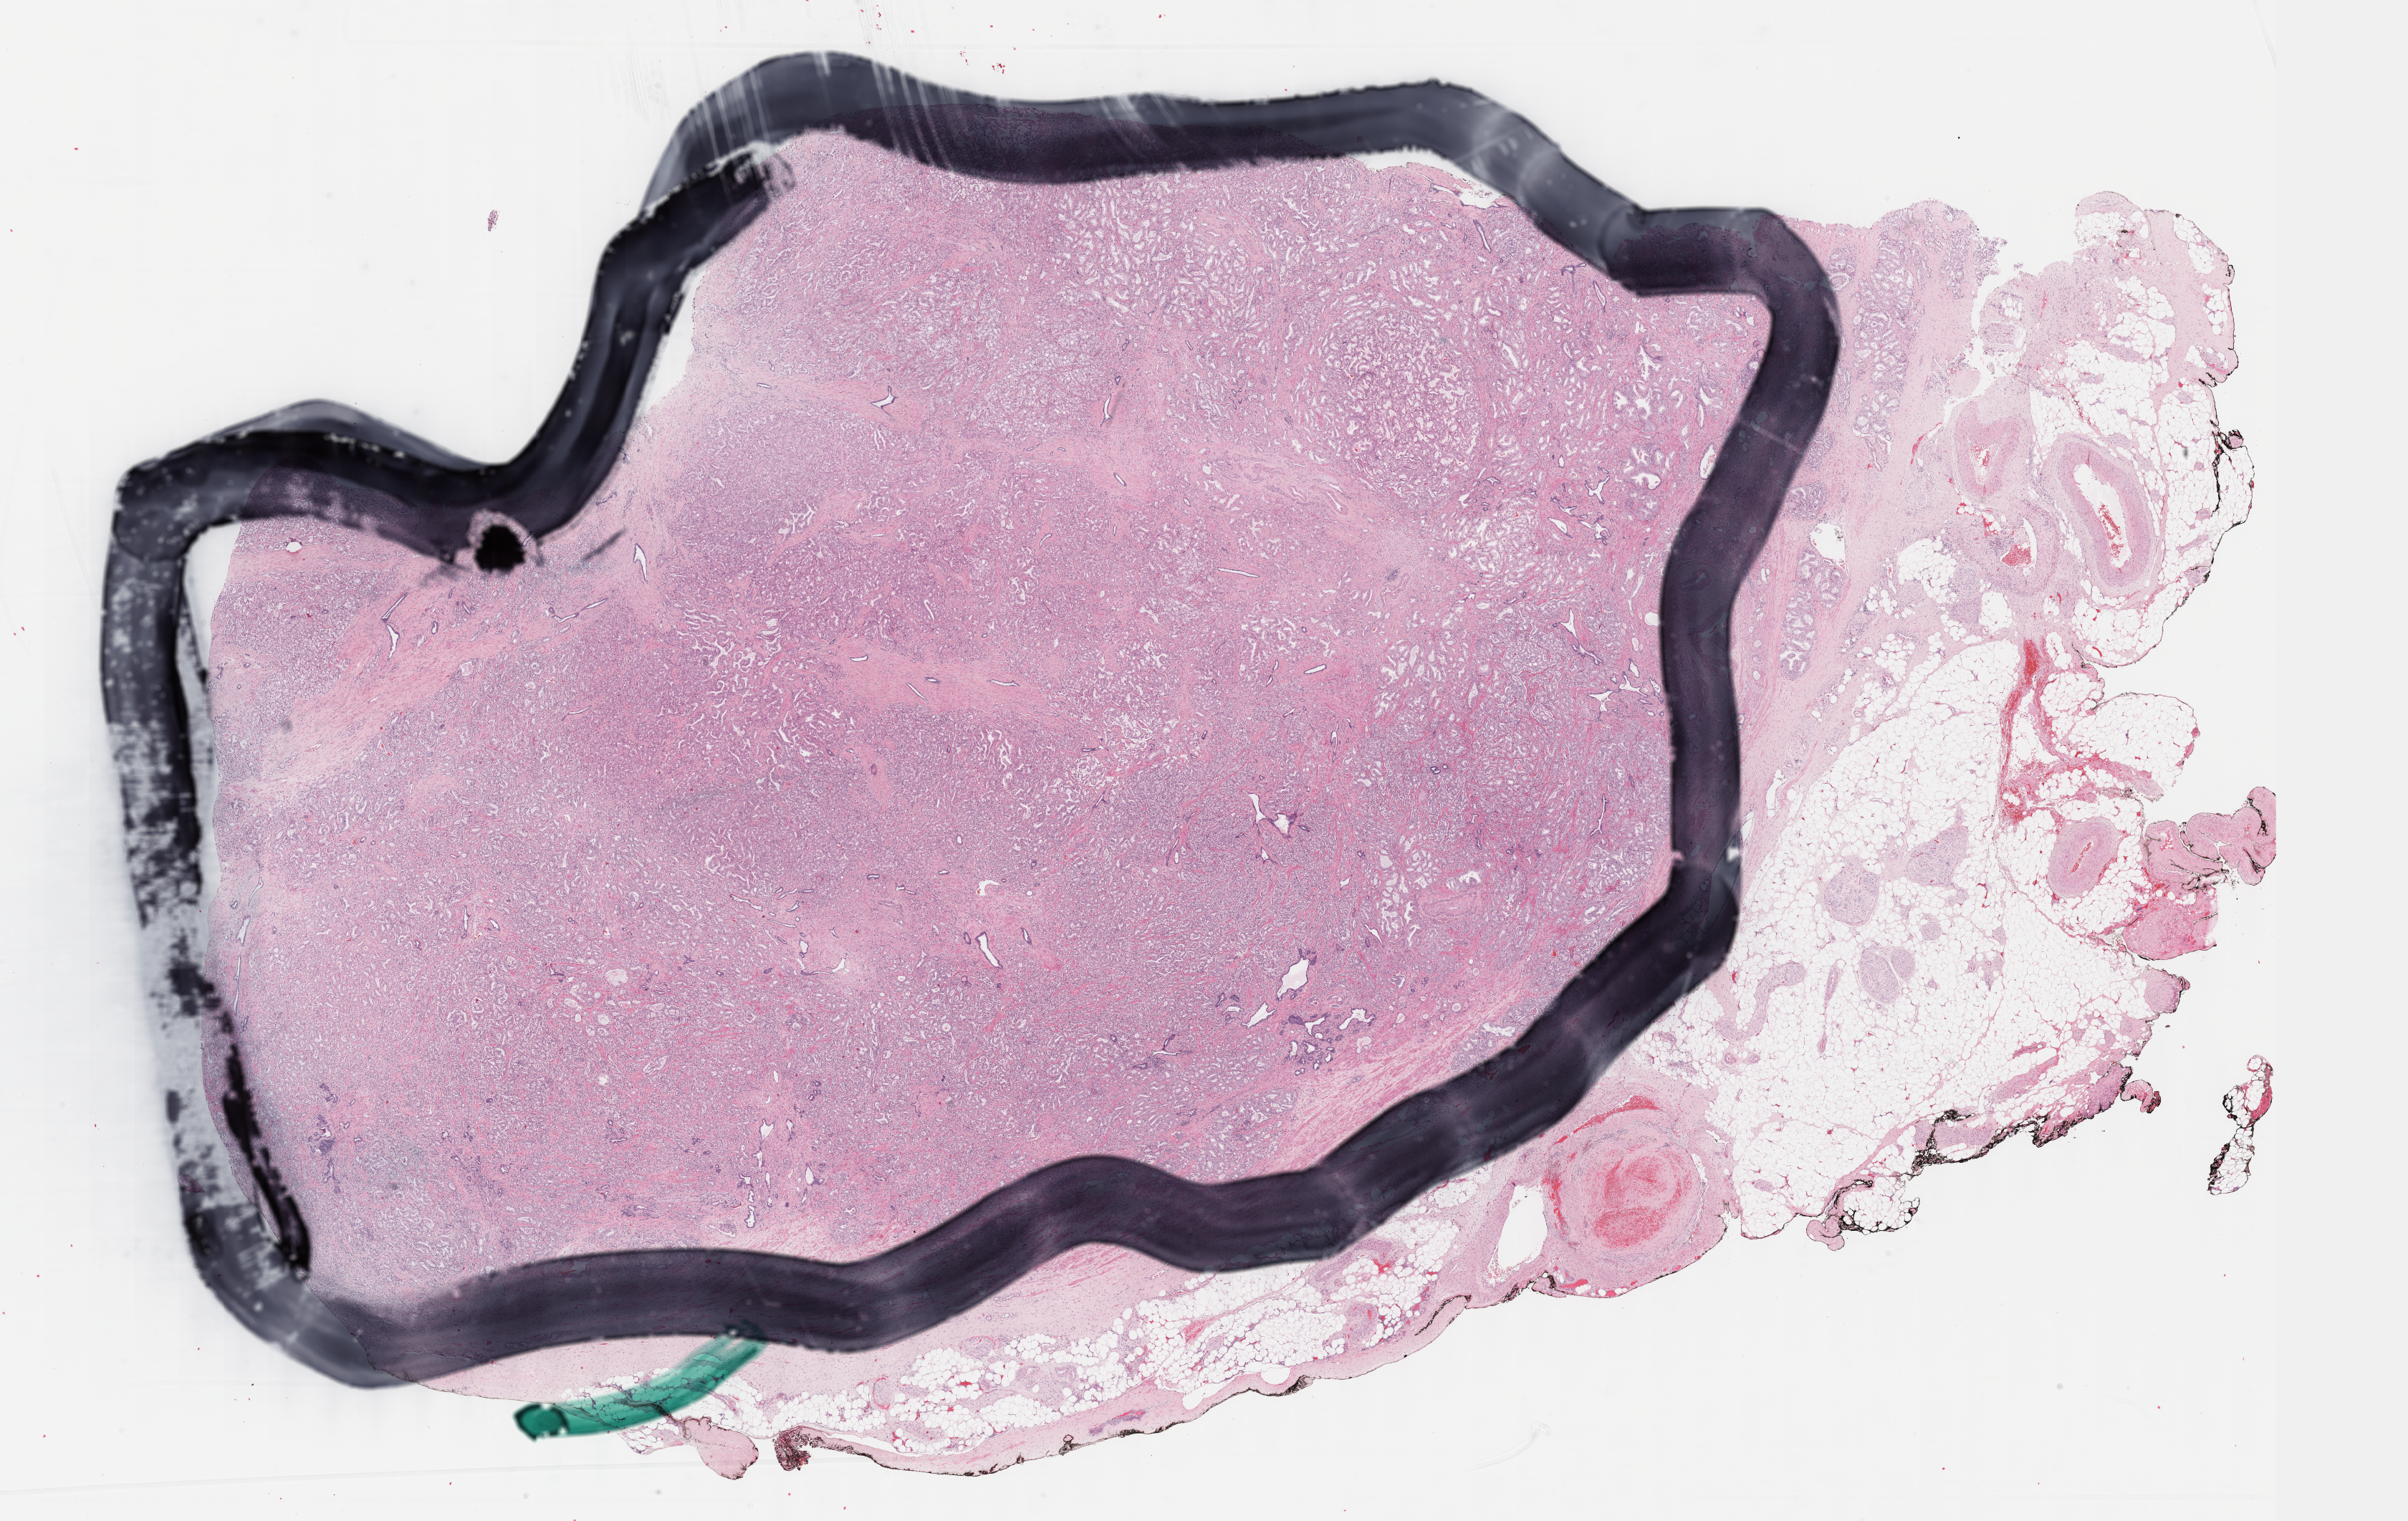
Whole-slide histology image, H&E-stained — low-resolution overview of the scanned area, about 26.7 x 16.9 mm (slide scanned at 40x). Formalin-fixed paraffin-embedded (FFPE) diagnostic section. Sample: primary tumour, prostate. Male, age 47 years at initial diagnosis.
Pathologic diagnosis: Adenocarcinoma, NOS.